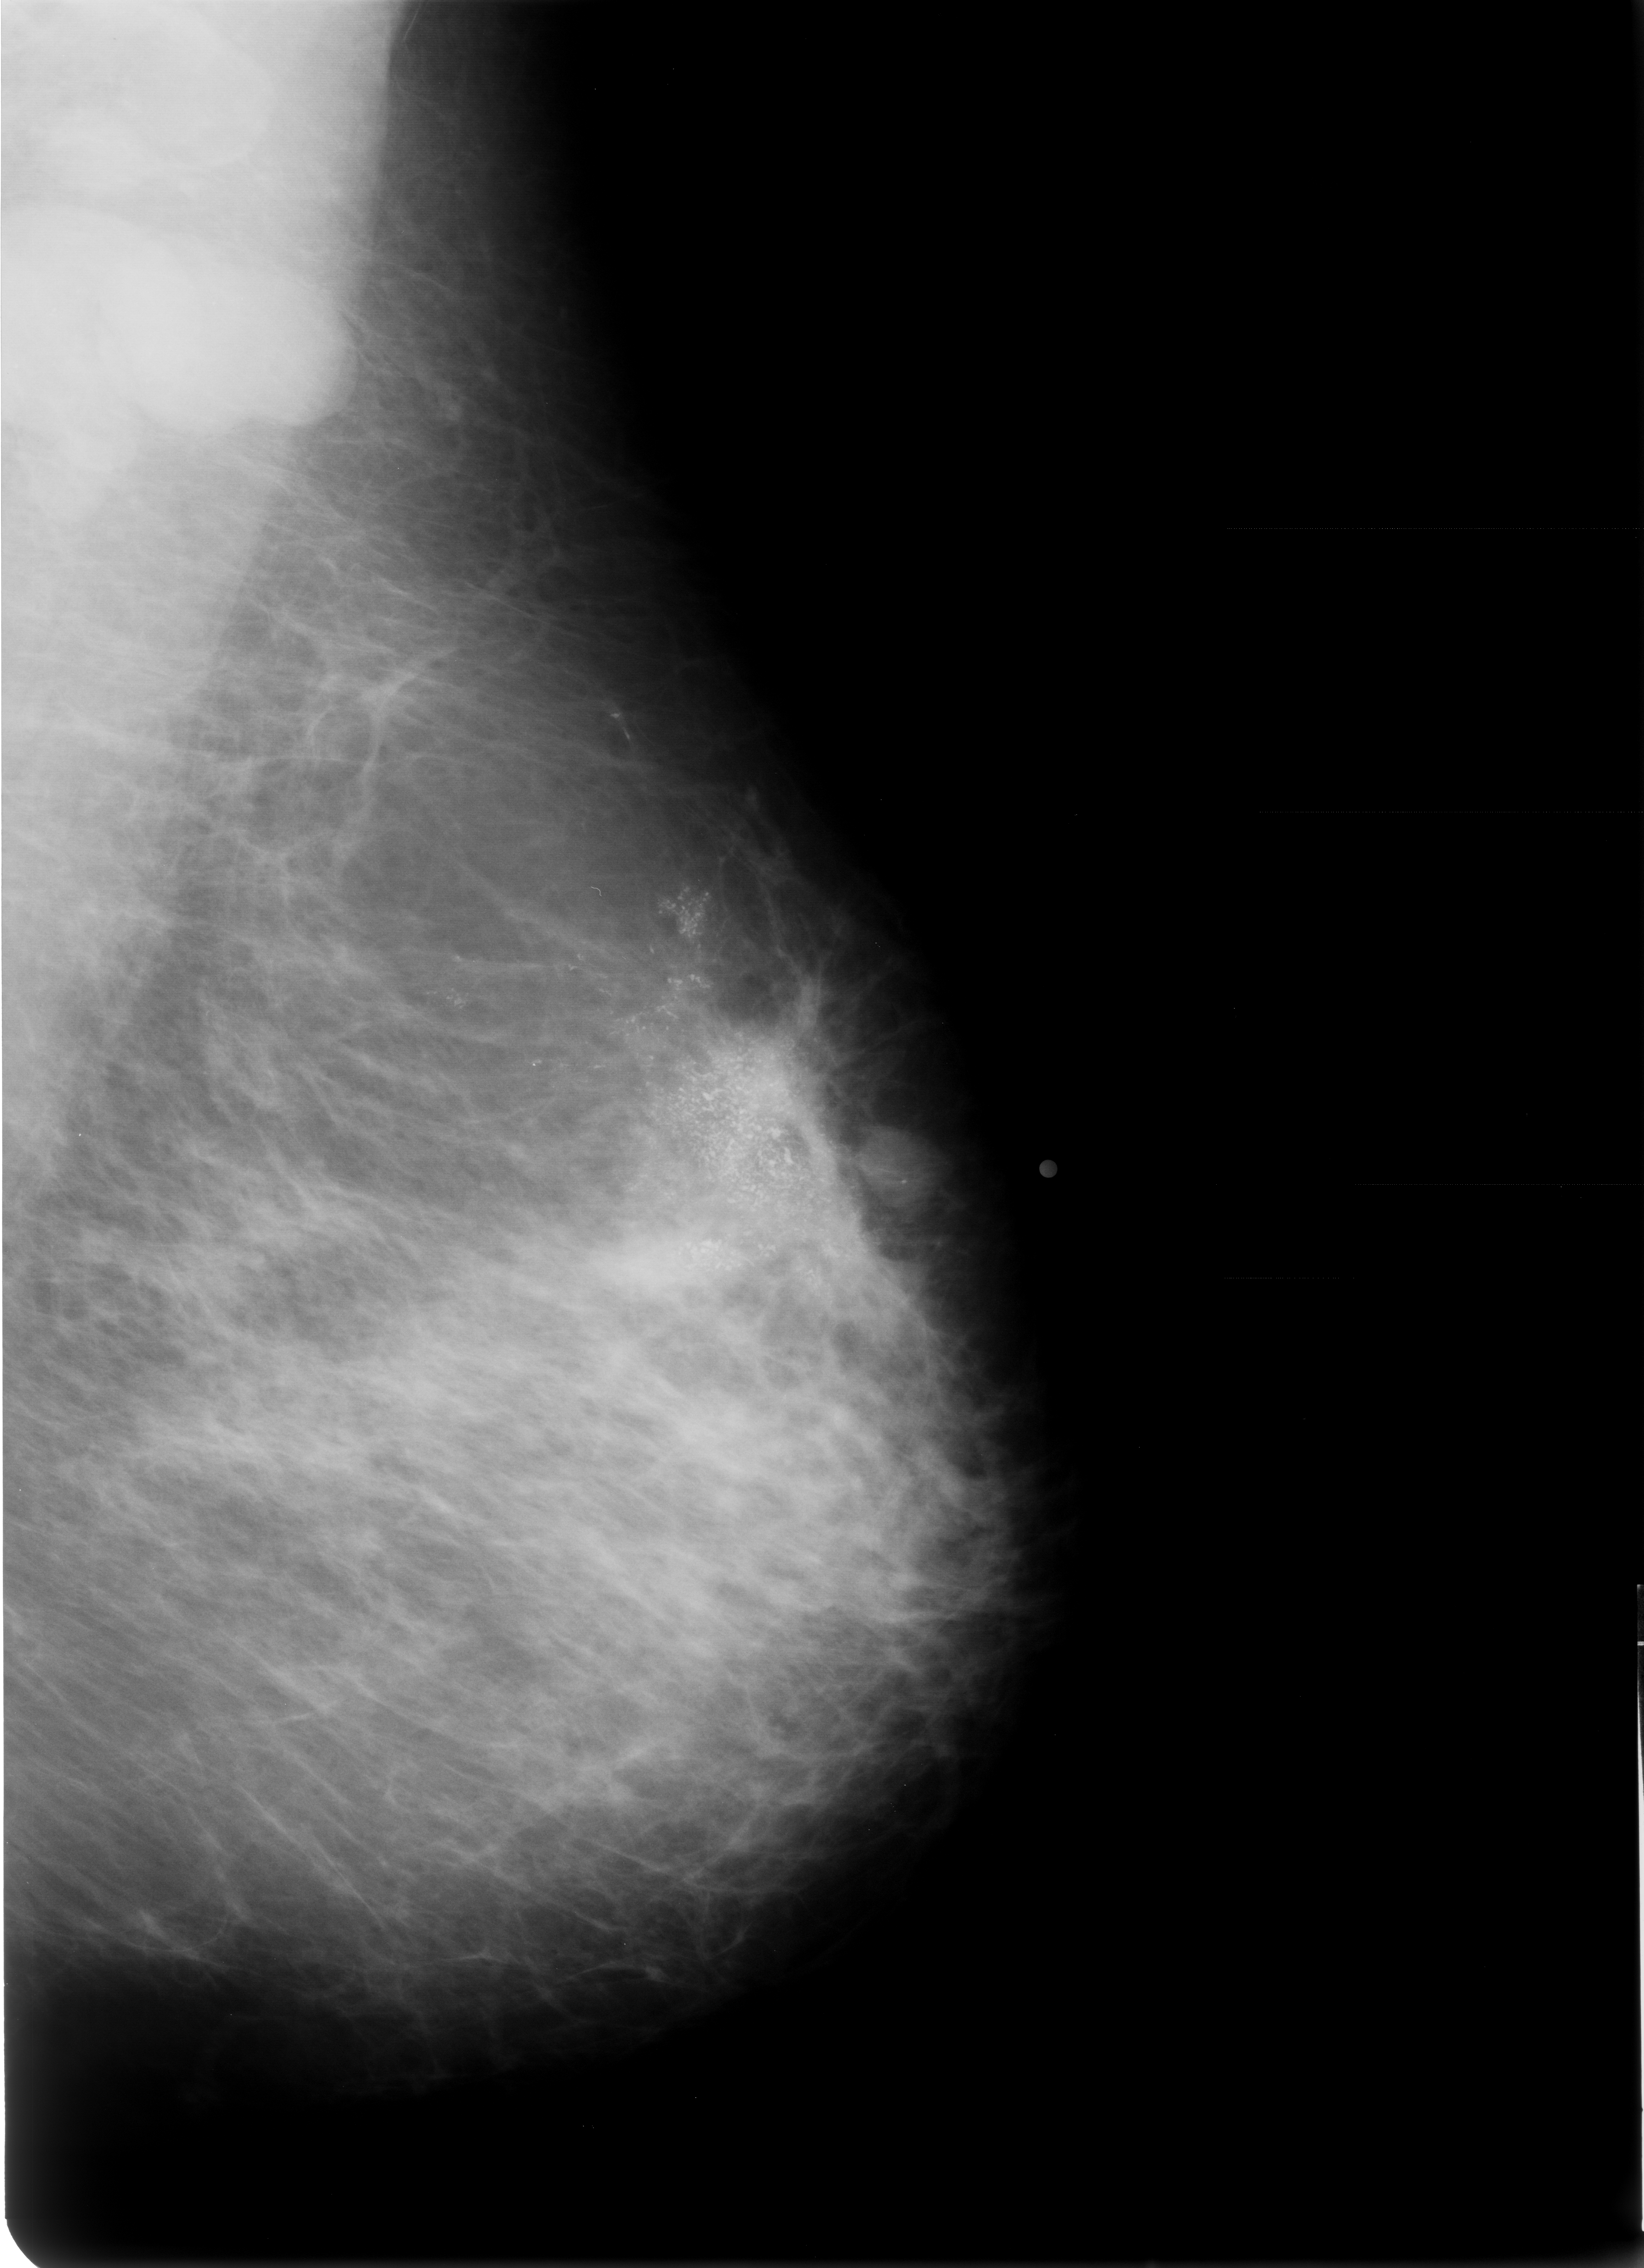
Digitized screen-film mammogram; left breast; mediolateral oblique (MLO) view; BI-RADS breast density category 2 (scale 1–4); 1644 × 2268 image matrix.
Expert-marked regions of interest on this film, with their recorded descriptors:
- calcifications, morphology pleomorphic, distribution segmental; BI-RADS assessment category 5; subtlety rating 5 on a 1 (subtle) to 5 (obvious) scale; pathology (as recorded): malignant: bounding box <315,642,977,1345> (left, top, right, bottom; pixels)